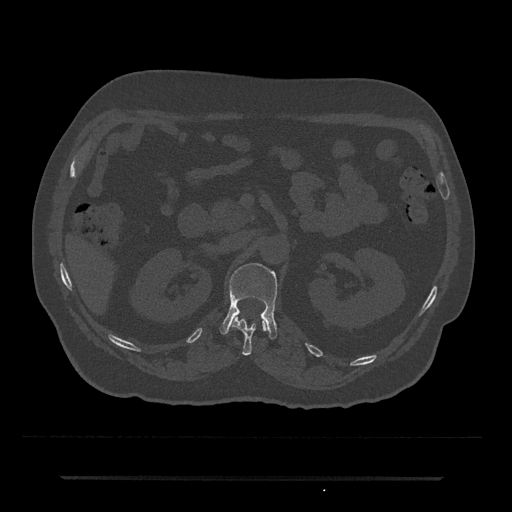
CT including the spine, one axial slice; position 92 of 797 along the scan axis; reconstruction kernel Br40s/3; bone window (W 1800 / L 400 HU); 0.5 mm slice thickness; 512 × 512 image matrix, field of view 437 × 437 mm. Male patient, age 69 years. Case-level facts recorded for this patient, not image findings: primary cancer: prostate.
Annotated regions visible in this slice (semi-automatically segmented with operator editing):
- L1 vertebra: box from (x=219, y=263) to (x=278, y=340) px
- T12 vertebra: (x=231, y=315)–(x=268, y=356)